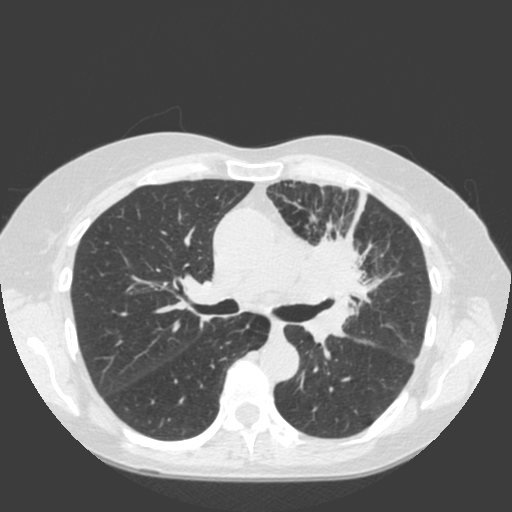
Low-dose screening chest CT, axial slice. Baseline screening round. Lung window (W 1500 / L -600 HU). 2 mm slice thickness. Standard (soft-tissue) reconstruction kernel (C). Slice 68 of 184 in the series. 512 × 512 image matrix, field of view 350 × 350 mm. Female participant, aged 66 years at enrolment.
Expert reader's lesion annotation, bounding box [x1, y1, x2, y2] px = [278, 210, 401, 320]. Screening reader's record for this exam (one nodule recorded; not confirmed to be the boxed lesion): non-calcified nodule or mass ≥4 mm, left upper lobe, 61 × 45 mm, spiculated (stellate) margins, soft tissue attenuation.